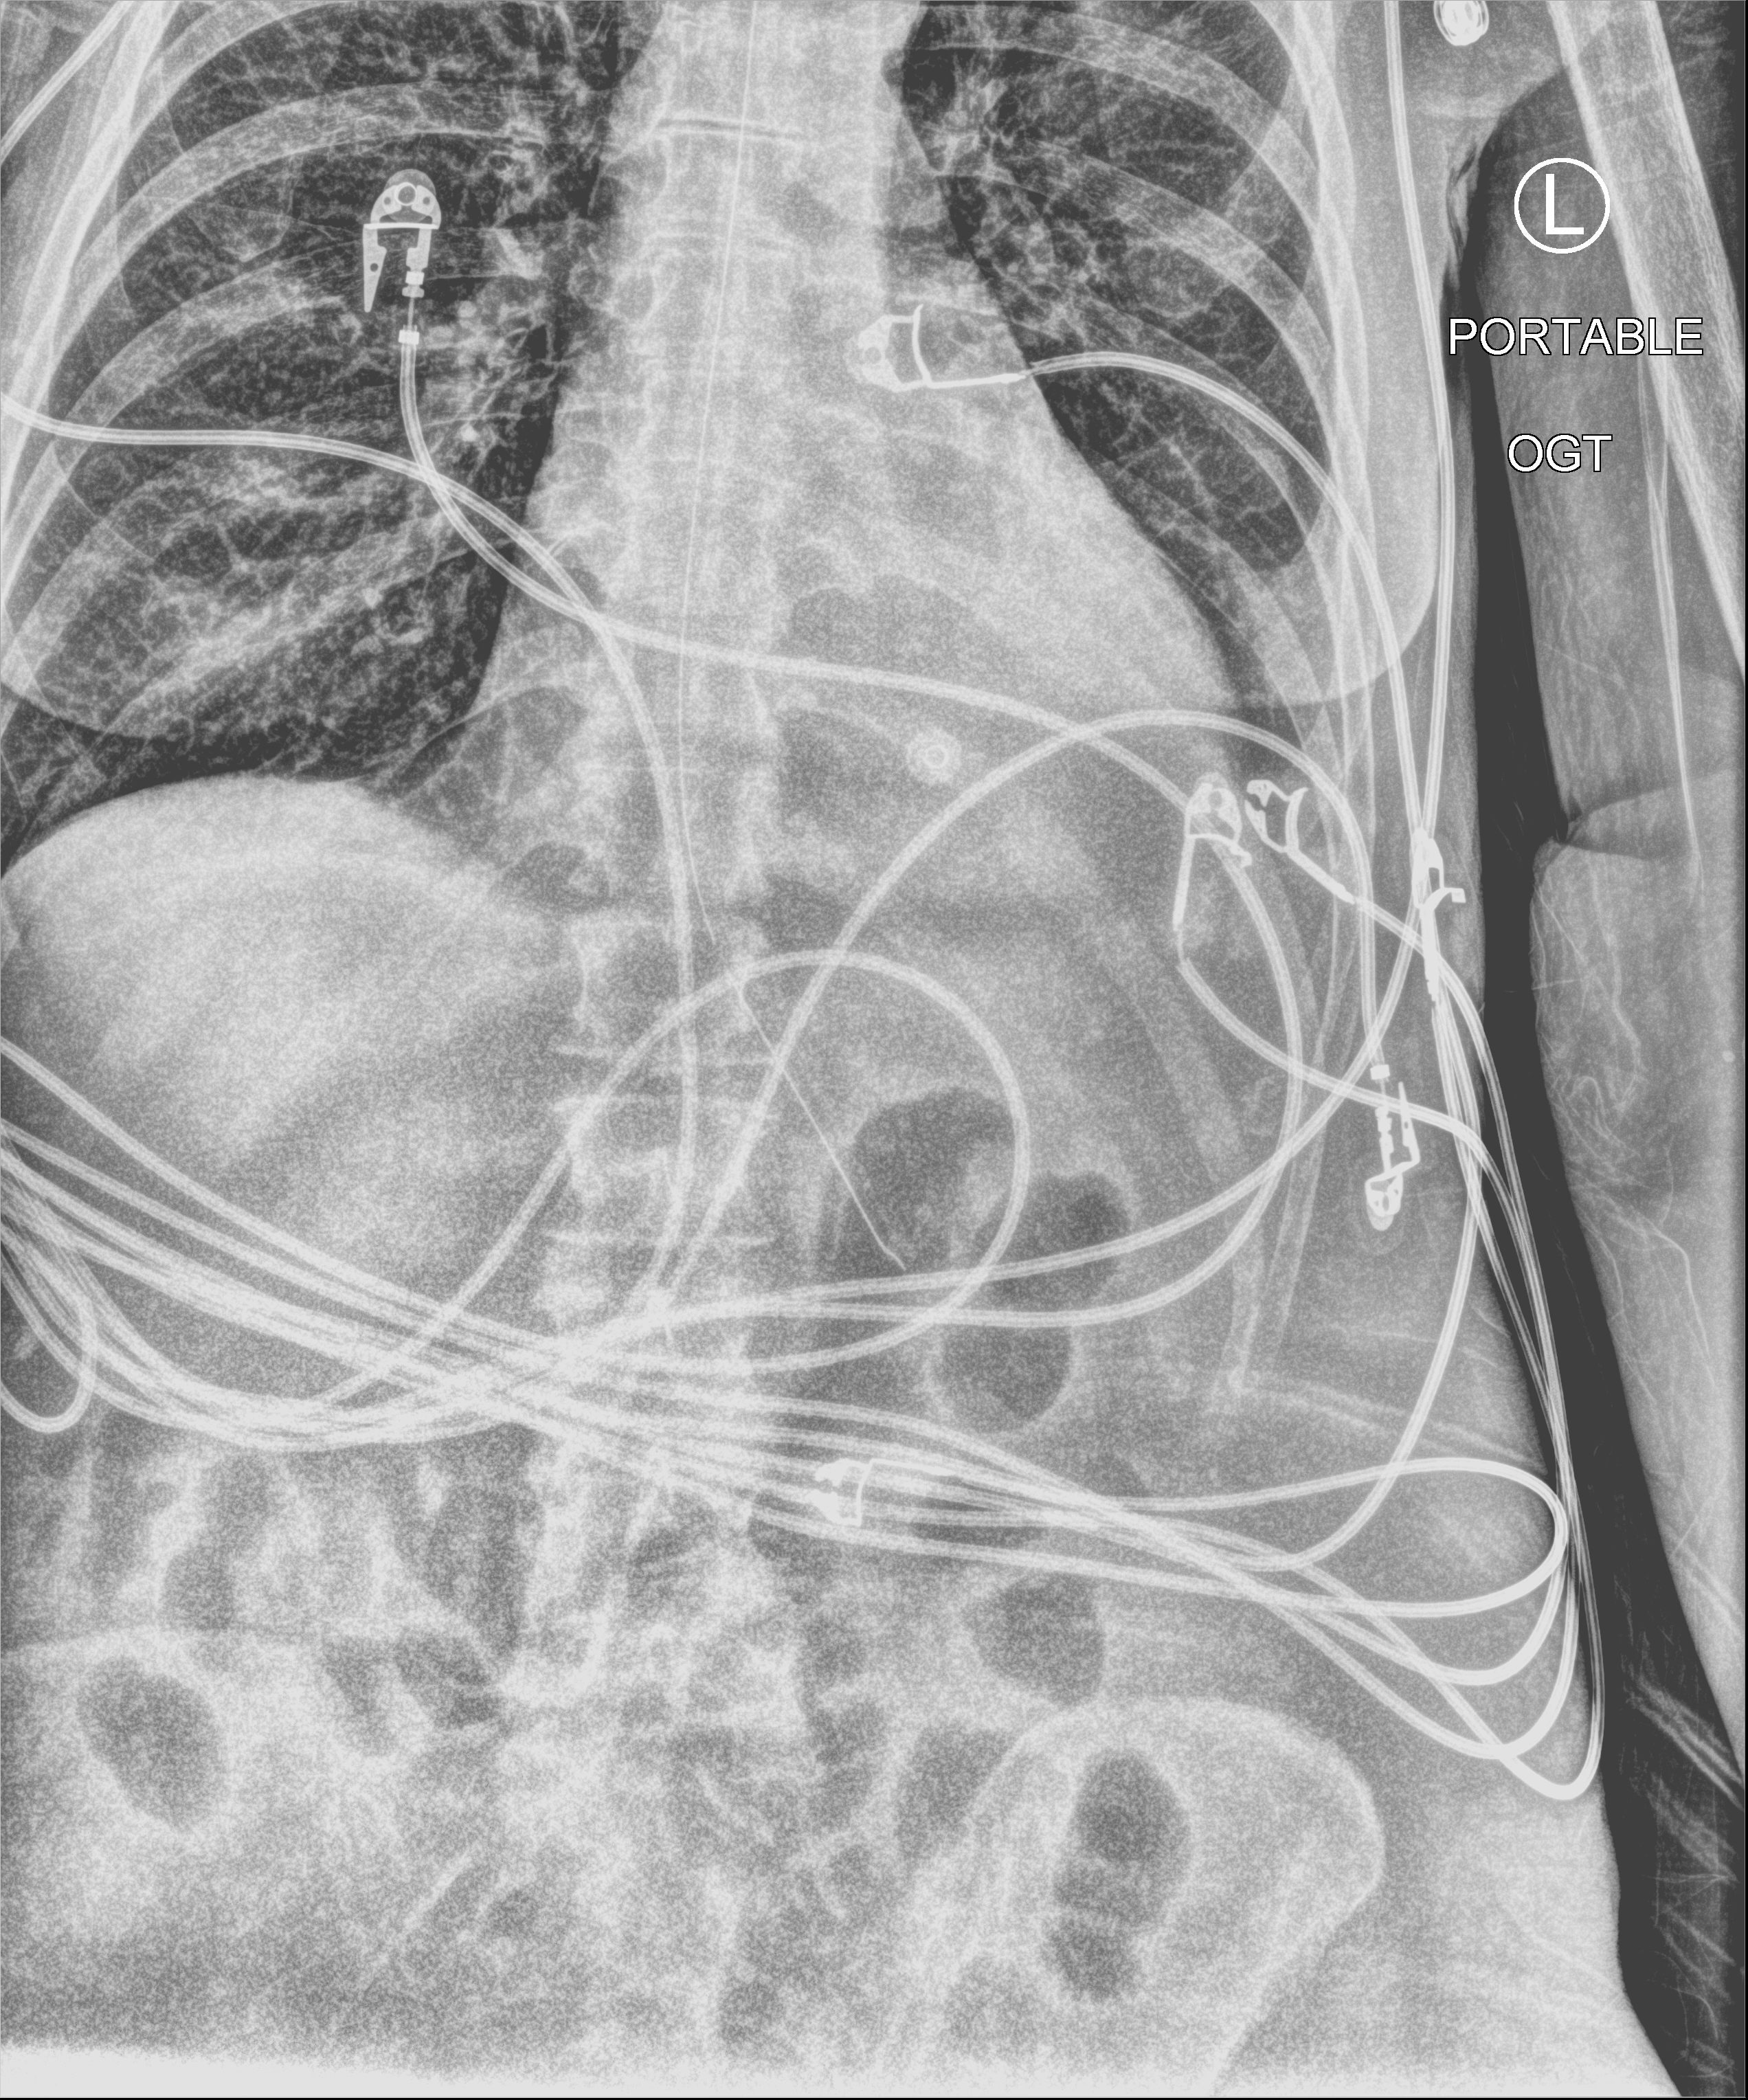
Bedside chest radiograph (computed radiography), anteroposterior (AP) projection. Patient hospitalised with COVID-19; female, aged 60–74 years.
Admission-level facts for this patient (not findings on this image; timing relative to this image not recorded): mechanically ventilated during this hospital stay: yes; admitted to intensive care during this hospital stay: yes.